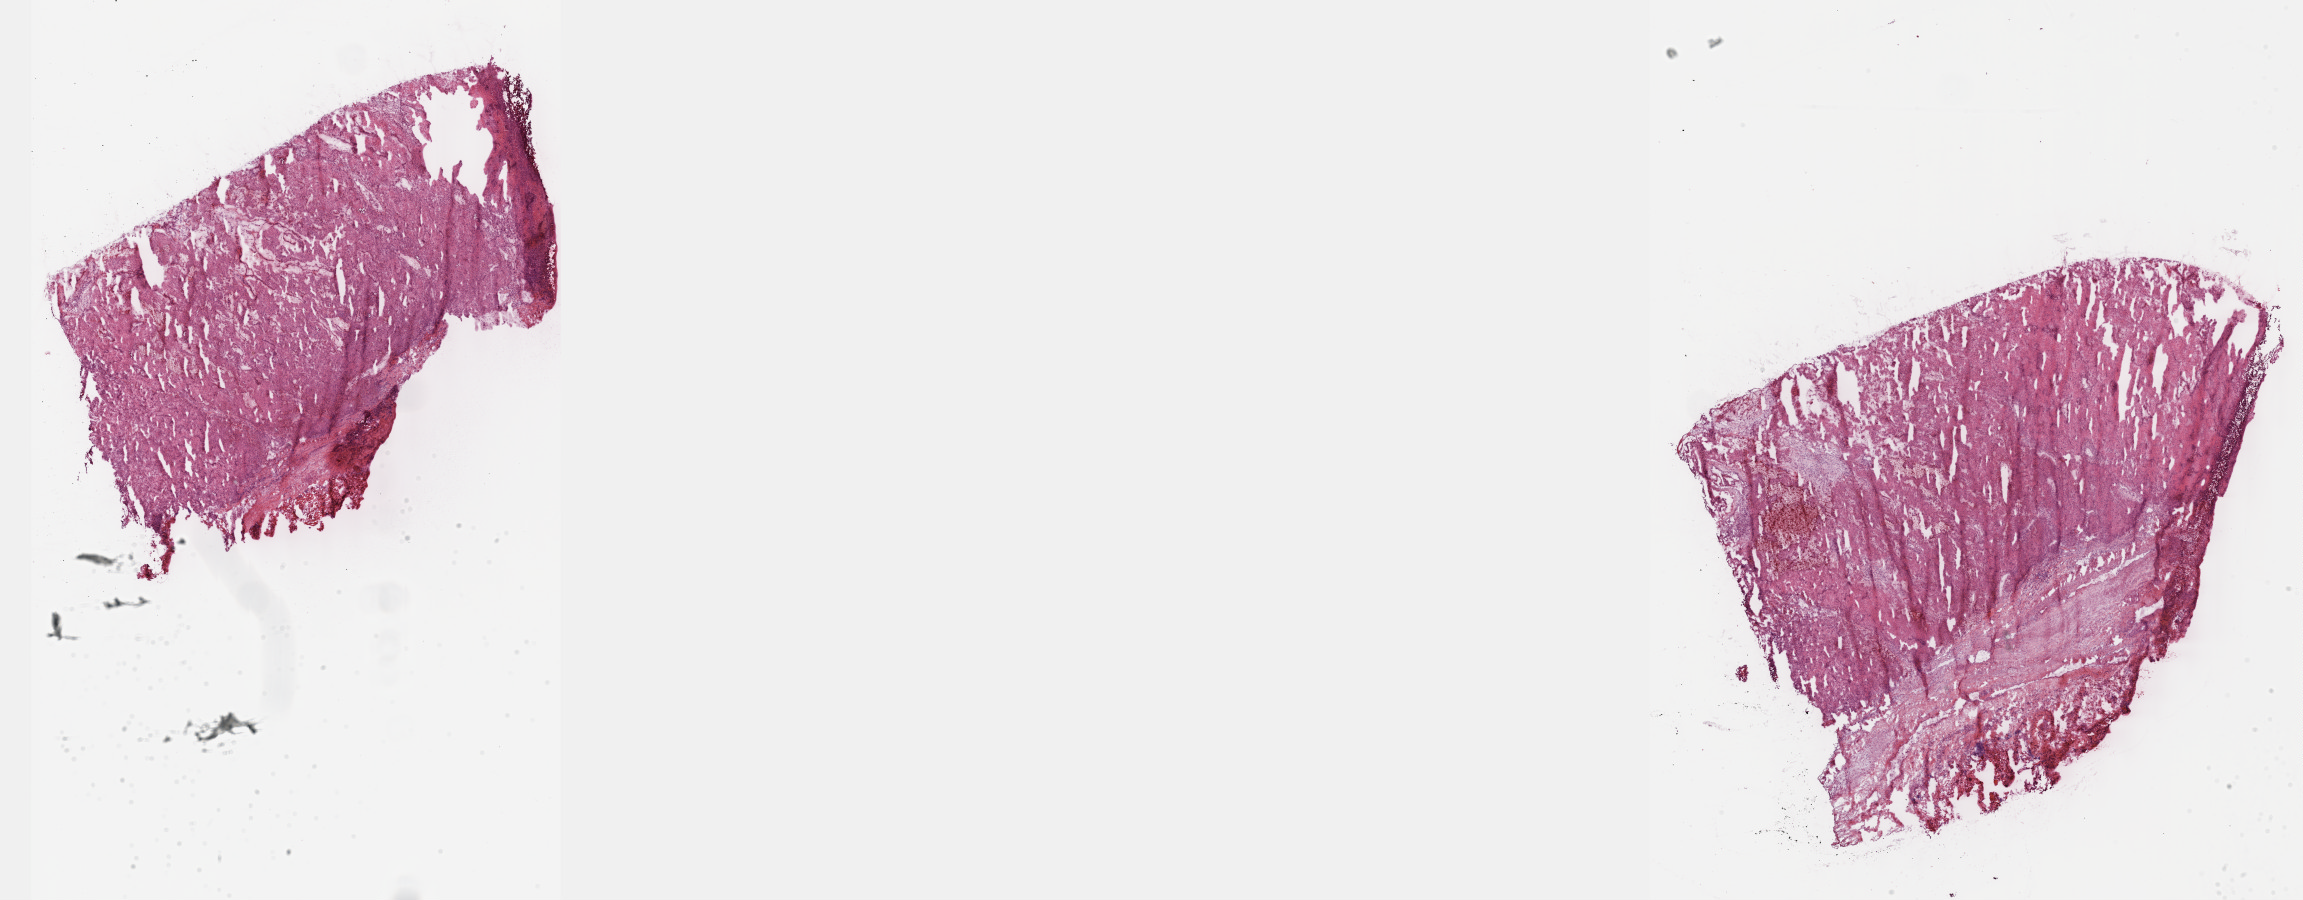
Whole-slide histology image, H&E, shown as a low-resolution overview of the whole scanned area (about 37.2 x 14.5 mm). Frozen section from the top of the tissue portion. Sample: primary tumour, adrenal gland. Male, age 23 years at initial diagnosis.
Diagnosis: Pheochromocytoma, malignant.